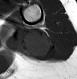
MRI of an extremity soft-tissue mass, one axial slice; slice 11 of 28 in the series (ordered by position); MR volume resampled by the dataset authors to the PET/CT grid (not the native acquisition matrix); 3.27 mm slice thickness; 77 × 79 image matrix, field of view 75 × 77 mm. Female patient. Case-level facts recorded for this patient, not image findings: histological type: malignant fibrous histiocytoma; grade: low; site of the primary tumour: left arm.
Structures marked on this image (expert contour drawn on MRI and transferred to this co-registered scan by the dataset authors):
- gross tumour volume (mass): bounding box [x1, y1, x2, y2] px = [21, 27, 57, 62]